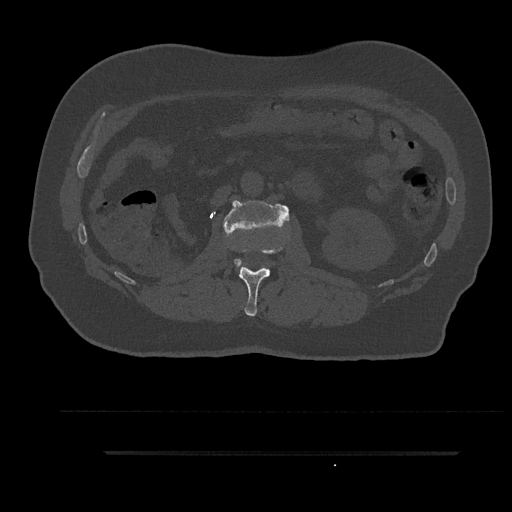
CT including the spine, one axial slice; slice 146 of 797 in the series (ordered by position); reconstruction kernel Br40s/3; 120 kVp; bone window (W 1800 / L 400 HU); 0.5 mm slice thickness; 512 × 512 image matrix, field of view 432 × 432 mm. Male patient, age 63 years. Case-level facts recorded for this patient, not image findings: primary cancer: renal; vertebrae with lytic lesions (as recorded): T8.
Outlined on this slice (semi-automatically segmented with operator editing):
- L1 vertebra: box from (x=239, y=246) to (x=284, y=316) px
- L2 vertebra: (x=222, y=200)–(x=289, y=266)